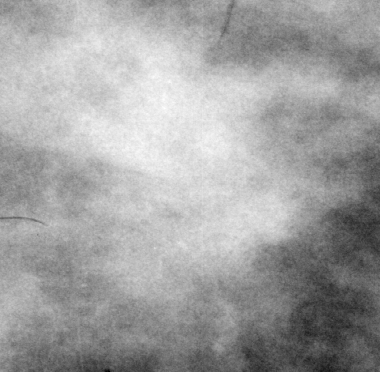
Region of interest cut from a scanned film mammogram (one marked finding); right breast; CC view; BI-RADS breast density category 2 (scale 1–4).
Marked abnormality: mass, shape irregular, margins ill defined; BI-RADS assessment category 4; pathology (as recorded): malignant.